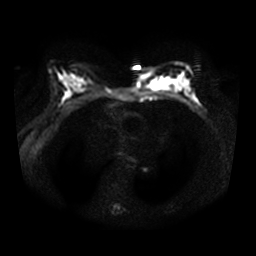
Breast MRI, one axial slice. Position 18 of 32 along the scan axis. Diffusion-weighted series; image 2 of 4 stored at this slice position (different b-values; order by instance number). 3 T. 5 mm slice thickness. 256 × 256 image matrix, field of view 340 × 340 mm. Female patient.
Outlined on this slice (manually delineated by an expert):
- tumour on diffusion-weighted imaging: bounding box [x1, y1, x2, y2] px = [154, 79, 175, 89]